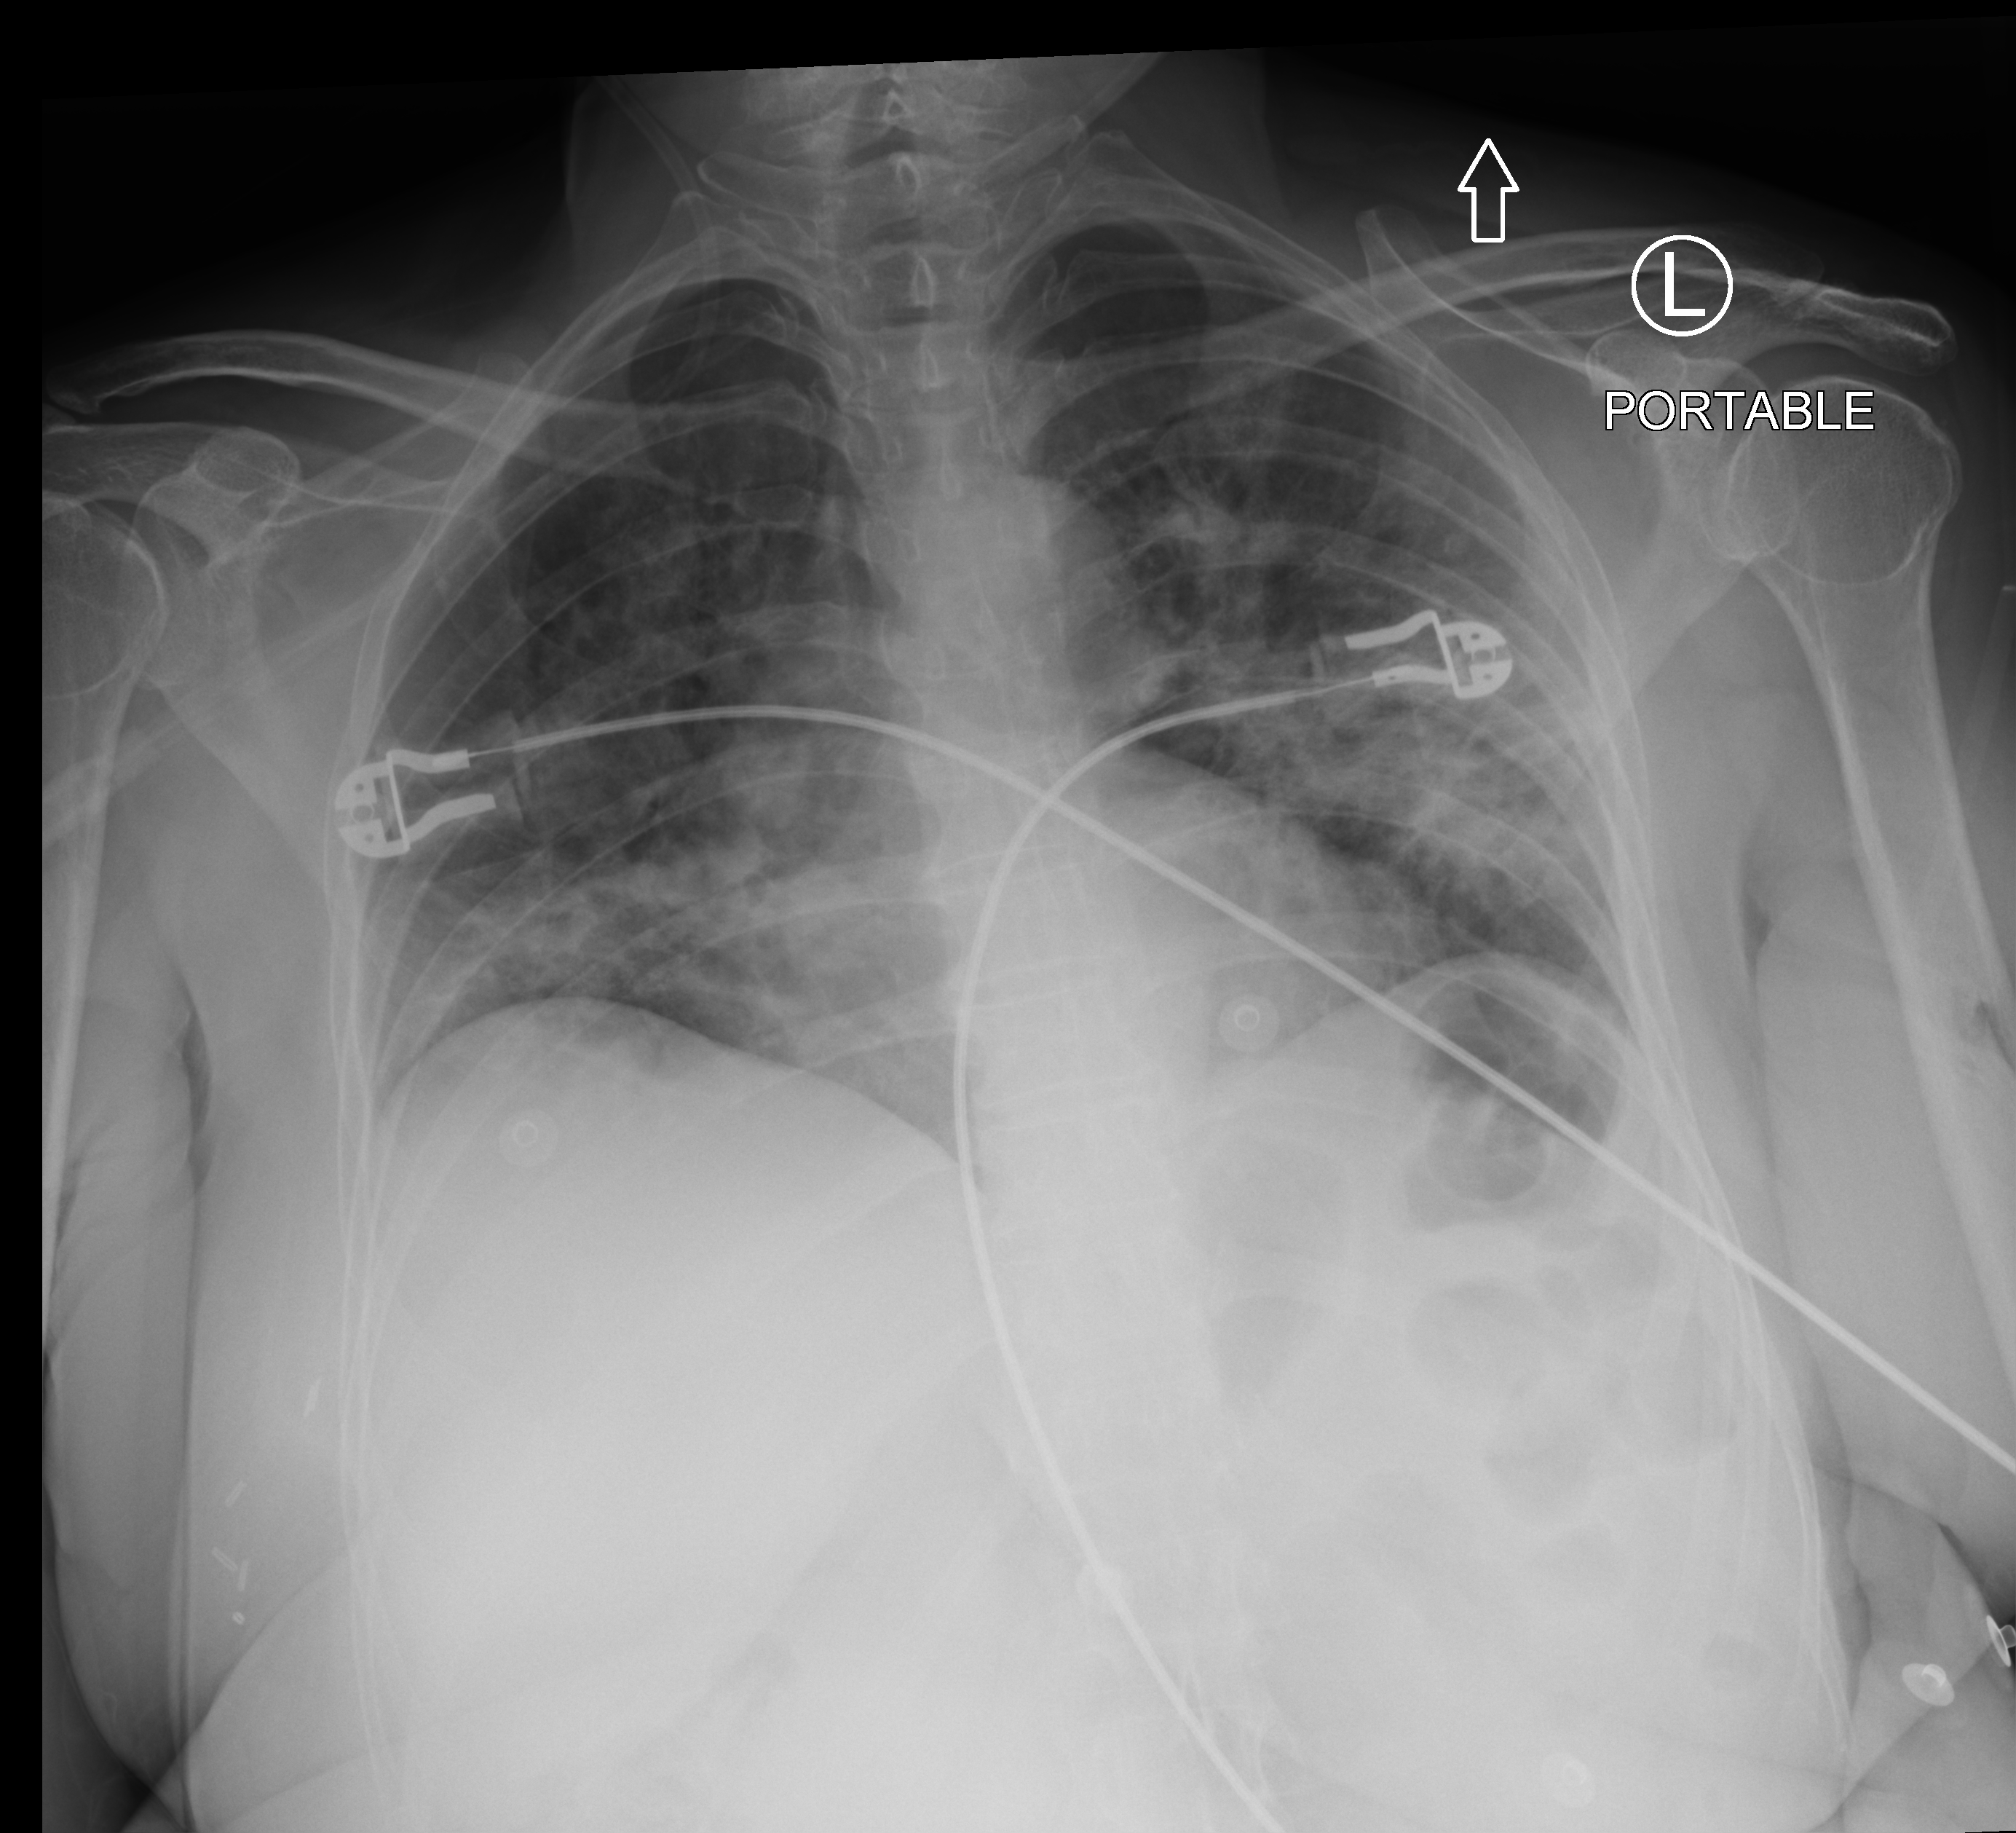
Portable chest radiograph; anteroposterior (AP) projection. Patient hospitalised with COVID-19; female, aged 60–74 years.
Hospital-stay facts (about this admission, not read from this image; timing relative to this image not recorded): mechanically ventilated during this hospital stay: no.